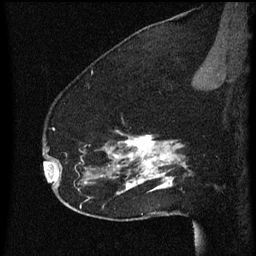
Breast MRI (dynamic contrast-enhanced), one sagittal slice. Position 44 of 60 along the scan axis. Dynamic contrast-enhanced series, image 2 of 3 at this slice position (ordered by acquisition). 1.5 T. TE 4.2 ms, TR 8 ms. 256 × 256 image matrix, field of view 180 × 180 mm. Patient: female, 52 years.
Structures marked on this image (semi-automatic segmentation, software-assisted and operator-edited):
- analysis volume of interest (the breast-tissue region the enhancement analysis was run in; not a lesion): bounding box (x1, y1, x2, y2) in pixels: (54, 130, 178, 207)
- tumour enhancement mask (voxels above the 70 % enhancement threshold inside the analysis volume of interest): (54, 130, 178, 195)